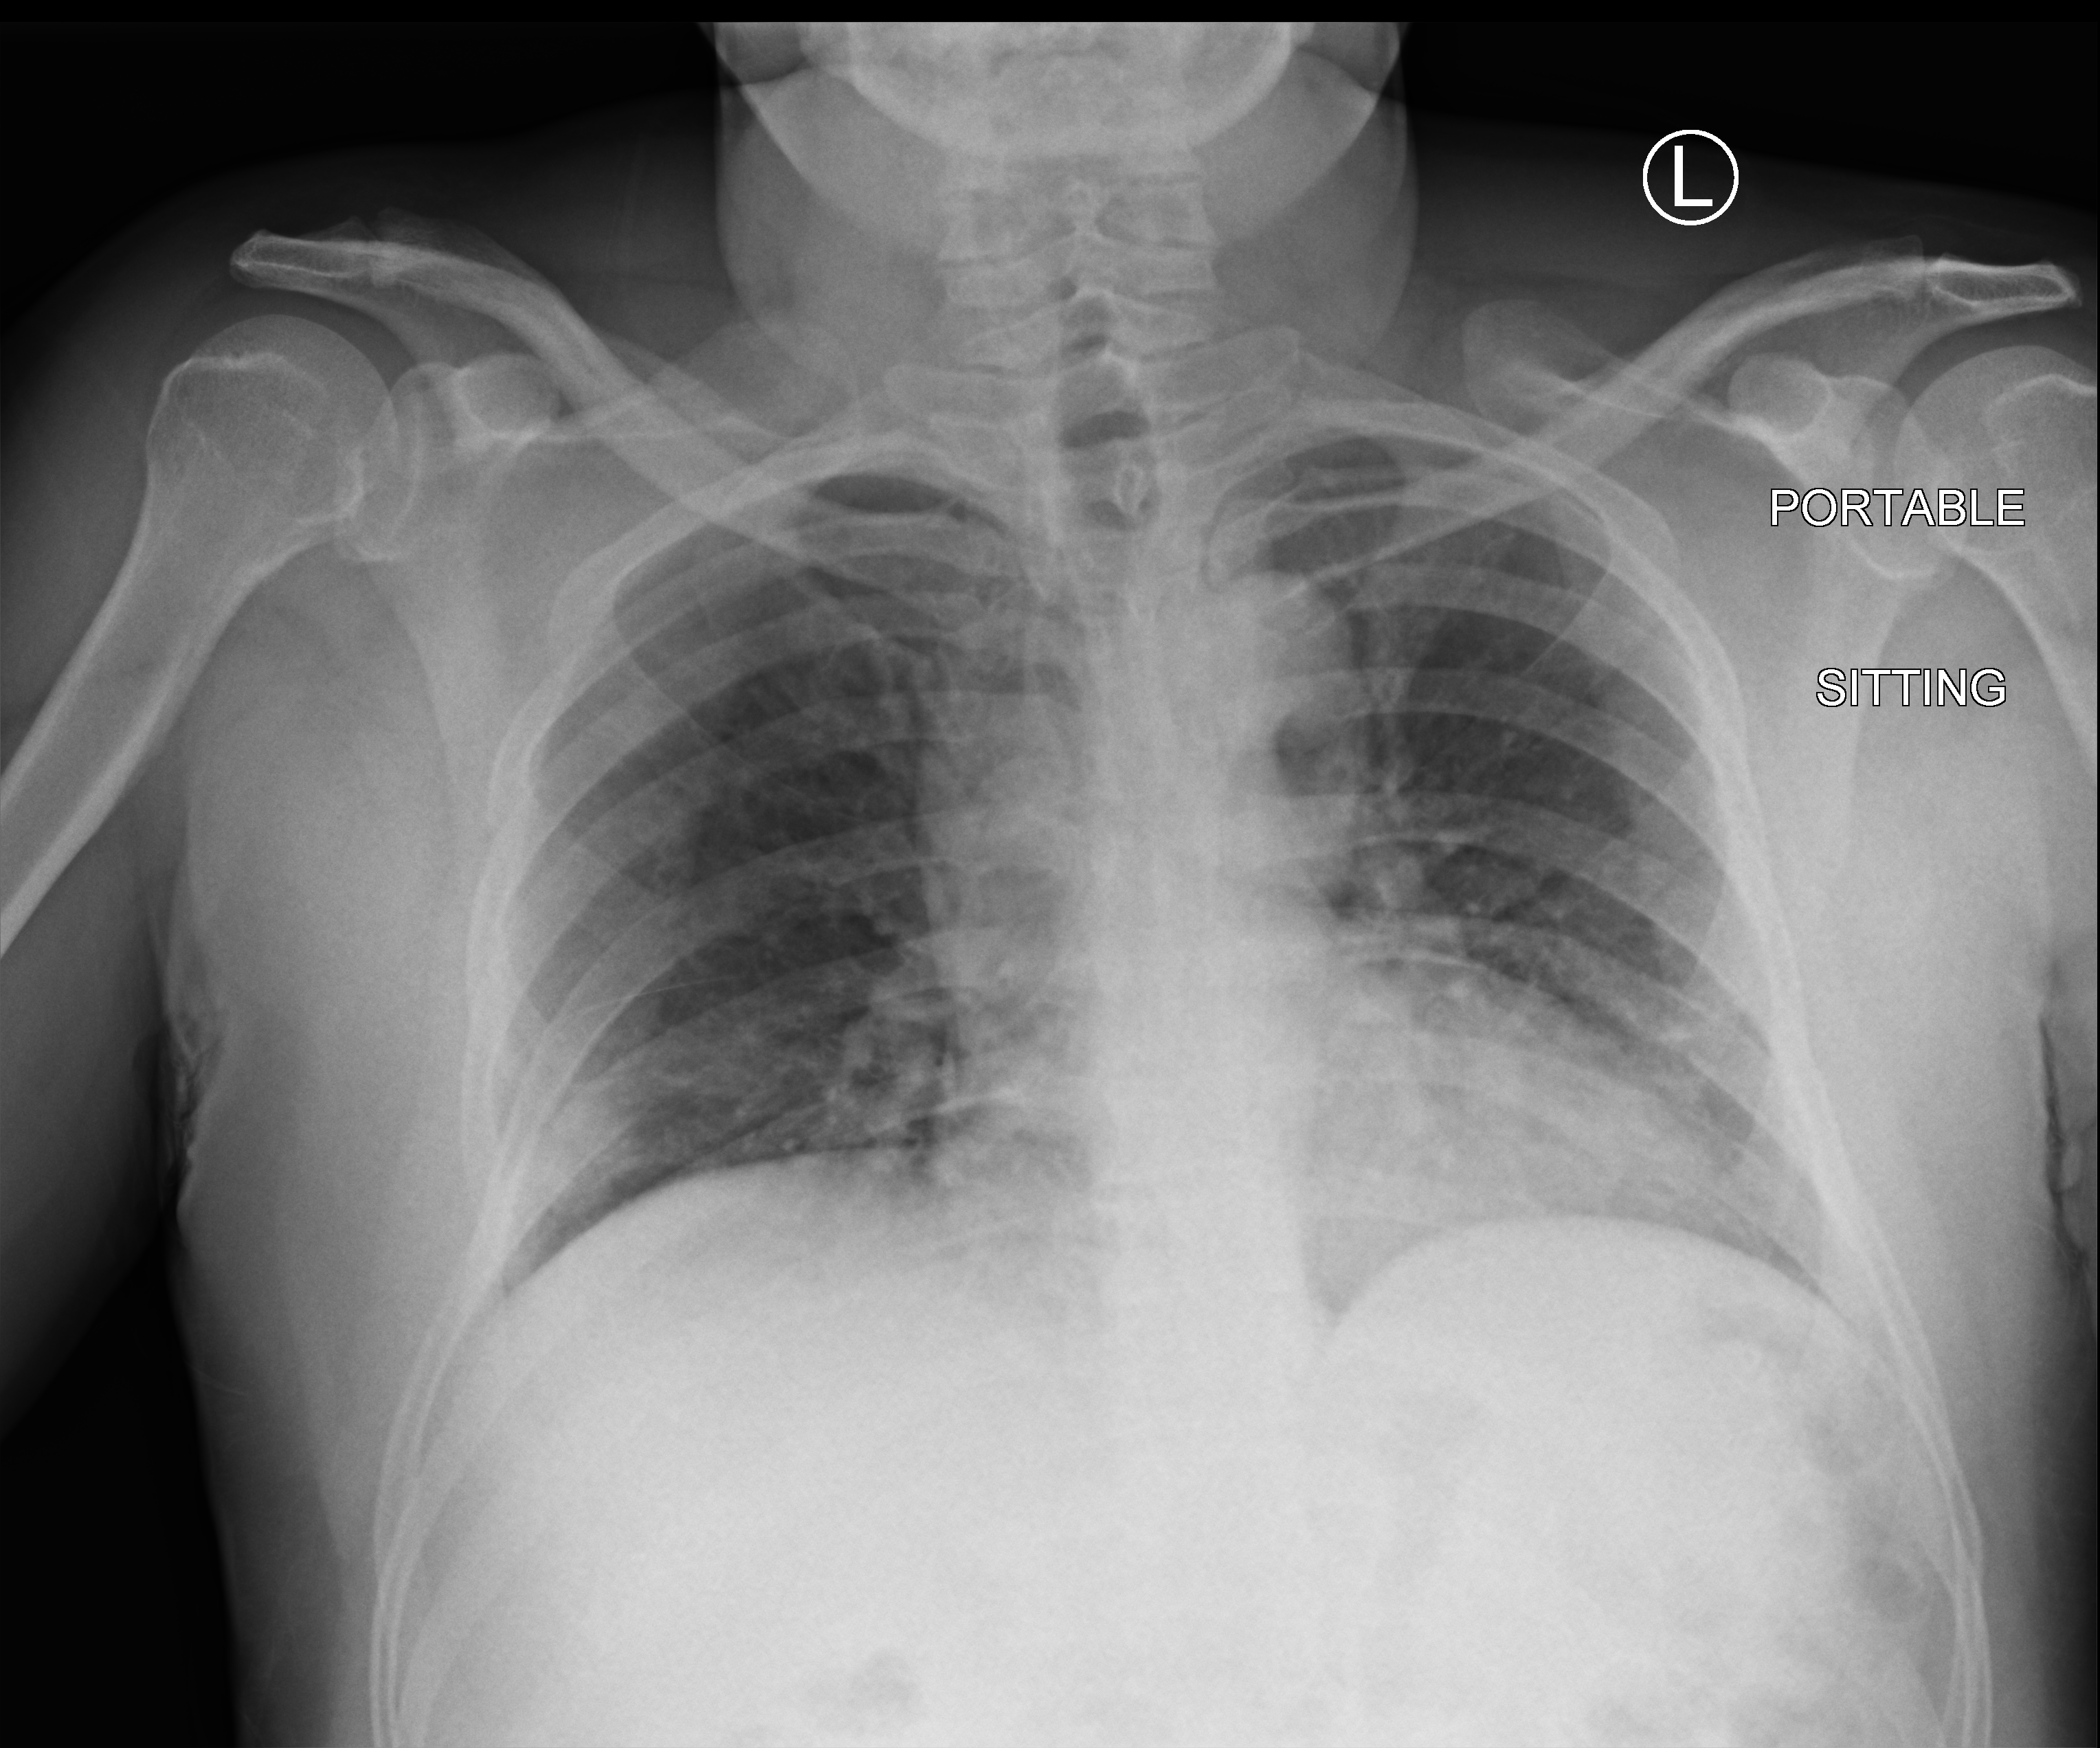
Chest X-ray (portable); anteroposterior (AP) projection. Male patient hospitalised with COVID-19, age 18–59 years.
Admission-level facts for this patient (not findings on this image; timing relative to this image not recorded): admitted to intensive care during this hospital stay: no.